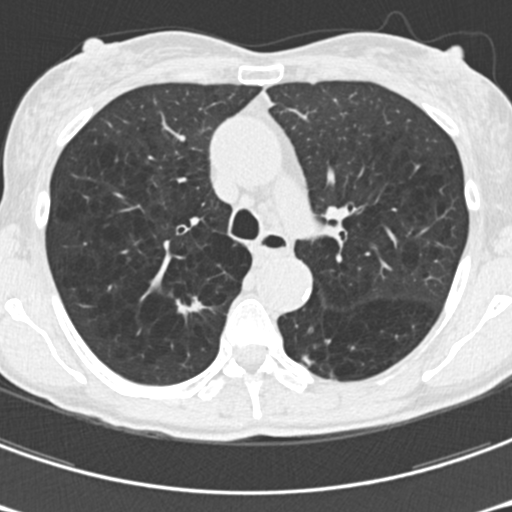
Low-dose screening chest CT, one axial slice; slice 118 of 176 in the series (ordered by position); lung window (W 1500 / L -600 HU); 2 mm slice thickness; 512 × 512 image matrix.
Structures marked on this image (expert manual segmentation):
- lesion 1 (tumor, upper lobe of right lung): bounding box [x1, y1, x2, y2] px = [177, 297, 205, 314]